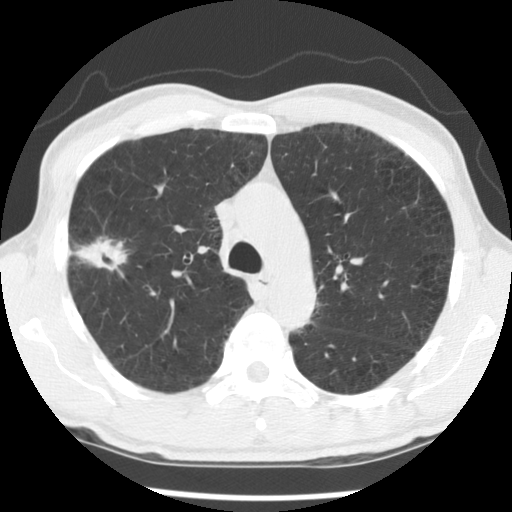
Low-dose screening chest CT, one axial slice; slice 91 of 138 in the series (ordered by position); reconstruction kernel STANDARD; 140 kVp; lung window (W 1500 / L -600 HU); 2.5 mm slice thickness; 512 × 512 image matrix, field of view 320 × 320 mm.
Annotated regions visible in this slice (outlined manually by an expert reader):
- lesion 1 (tumor, upper lobe of right lung): bounding box <74,237,128,271> (left, top, right, bottom; pixels)